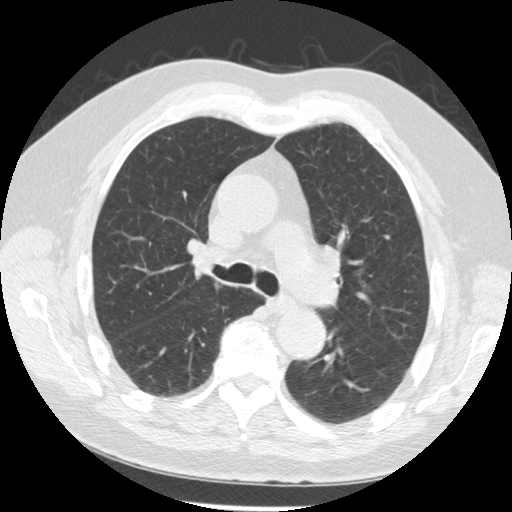
Low-dose screening chest CT, one axial slice. Slice 168 of 259 in the series (ordered by position). 120 kVp. Lung window (W 1500 / L -600 HU). 2.5 mm slice thickness. 512 × 512 image matrix, field of view 355 × 355 mm.
Structures marked on this image (expert manual segmentation):
- lesion 2 (tumor, hilum of right lung): bounding box <194,242,213,272> (left, top, right, bottom; pixels)